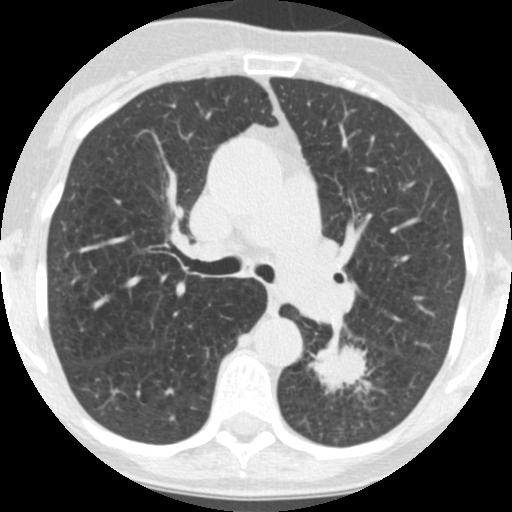
Chest CT (low-dose screening protocol), one axial image, third screening round (two years after baseline), lung window (W 1500 / L -600 HU), 2.5 mm slice thickness, standard (soft-tissue) reconstruction kernel (STANDARD), slice 61 of 171 in the series. Female, age 71 years at enrolment. Current smoker at enrolment.
Expert-annotated lung lesion, bounding box (x1, y1, x2, y2) in pixels: (305, 325, 384, 409). The screening reader recorded 2 non-calcified nodules or masses ≥4 mm on this exam; which of them this box marks is not recorded. Later outcome: lung cancer diagnosed 26 days after this screen — squamous cell carcinoma, NOS, left lower lobe, poorly differentiated (G3), stage IB (AJCC 6th edition), 40 mm at pathology.